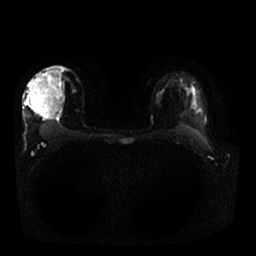
Breast MRI, one axial slice. Slice 14 of 25 in the series (ordered by position). Diffusion-weighted series; image 2 of 4 stored at this slice position (different b-values; order by instance number). 1.5 T. 4 mm slice thickness. 256 × 256 image matrix. Female patient.
Structures marked on this image (manually delineated by an expert):
- tumour on diffusion-weighted imaging: bounding box (x1, y1, x2, y2) in pixels: (56, 113, 62, 118)